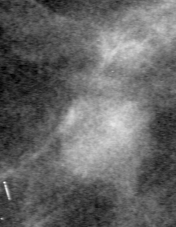
Crop from a digitized film mammogram around one marked abnormality; left breast; MLO view.
Marked abnormality: mass, shape oval, margins circumscribed; BI-RADS assessment category 4; pathology (as recorded): malignant.